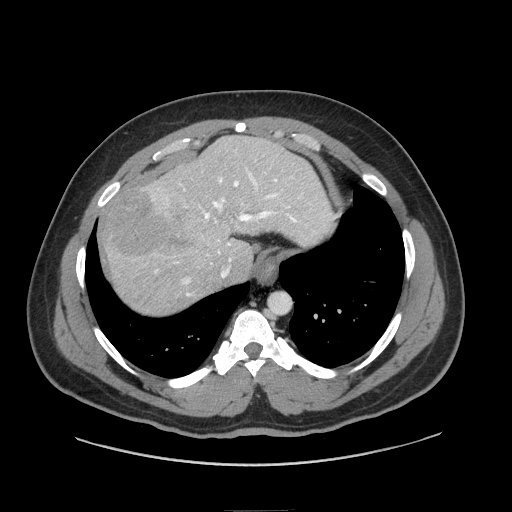
Contrast-enhanced abdominal CT (liver protocol), one axial slice. Slice 64 of 87 in the series (ordered by position). Reconstruction kernel STANDARD. 140 kVp. Soft-tissue window (W 400 / L 40 HU). 2.5 mm slice thickness. 512 × 512 image matrix. From the clinical record (not read from this slice): diagnosis: hepatocellular carcinoma (patient treated with transarterial chemoembolisation; whether this scan precedes or follows treatment is not stated here); TNM stage (as recorded): Stage-II; Child-Pugh class: A; tumour differentiation: moderately differentiated.
Structures marked on this image (semi-automatic segmentation, software-assisted and operator-edited):
- liver parenchyma outside the tumour (the mass and vessels are separate outlines, so this box may not span the whole liver): bounding box <102,136,334,314> (left, top, right, bottom; pixels)
- mass: <101,183,193,262>
- liver vessels: <155,168,298,296>